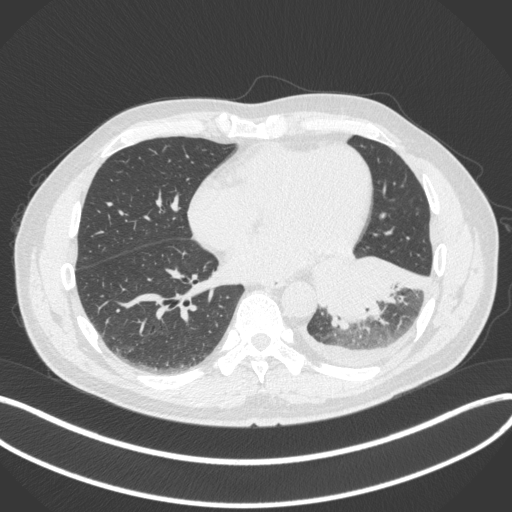
Chest CT, one axial slice; slice 138 of 350 in the series (ordered by position); lung window (W 1500 / L -600 HU); 1 mm slice thickness; 512 × 512 image matrix. Patient: male, 58 years. From the clinical record (not read from this slice): clinical TNM (as recorded): T3 N1 M1b.
Annotated regions visible in this slice (bounding box drawn by a radiologist):
- lung tumour (recorded histology: small cell carcinoma): bounding box [x1, y1, x2, y2] px = [313, 251, 431, 334]